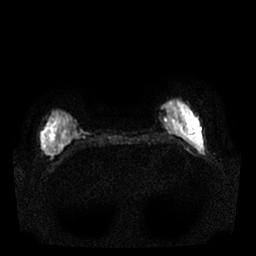
Breast MRI, one axial slice; position 5 of 25 along the scan axis; diffusion-weighted series; image 2 of 4 stored at this slice position (different b-values; order by instance number); 1.5 T; 256 × 256 image matrix, field of view 340 × 340 mm. Female patient.
Annotated regions visible in this slice (expert manual segmentation):
- tumour on diffusion-weighted imaging: box from (x=44, y=141) to (x=52, y=154) px